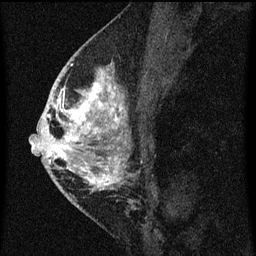
Breast MRI (dynamic contrast-enhanced), one sagittal slice. Slice 32 of 60 in the series (ordered by position). Dynamic contrast-enhanced series, image 2 of 3 at this slice position (ordered by acquisition). 1.5 T. TE 4.2 ms, TR 8 ms. 256 × 256 image matrix, field of view 180 × 180 mm. Female patient, age 46 years.
Structures marked on this image (semi-automatic segmentation, software-assisted and operator-edited):
- analysis volume of interest (the breast-tissue region the enhancement analysis was run in; not a lesion): bounding box [x1, y1, x2, y2] px = [48, 68, 128, 195]
- tumour enhancement mask (voxels above the 70 % enhancement threshold inside the analysis volume of interest): [48, 68, 126, 191]